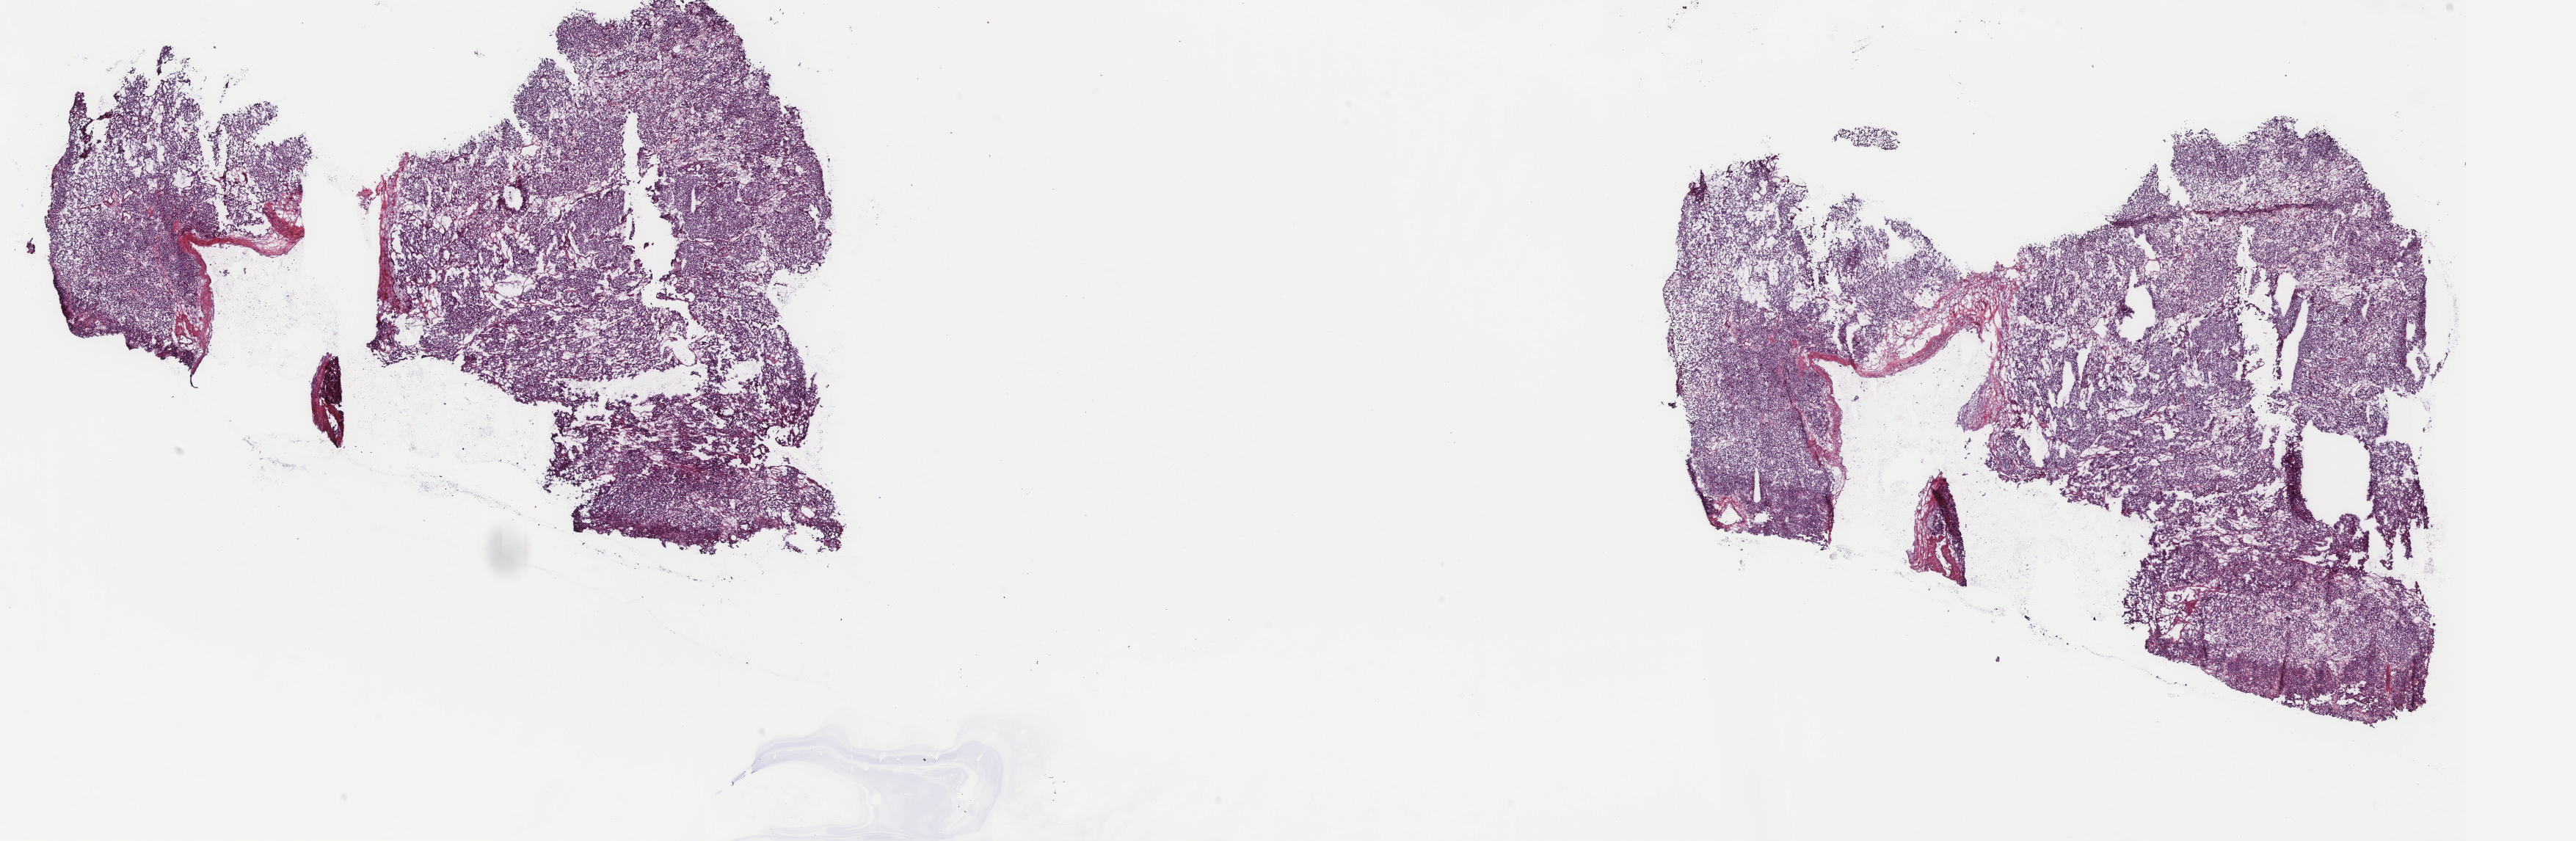
Hematoxylin and eosin (H&E) stained whole-slide image, low-resolution overview of the scanned area, about 27.9 x 9.1 mm; frozen section from the top of the tissue portion; sample: primary tumour, adrenal gland. Patient: male, age at initial diagnosis 48 years. Composition of this section per pathologist review: tumour cells 100%, tumour nuclei 80%, normal cells 0%, stromal cells 0%, necrosis 0%. Inflammatory infiltration, as recorded: lymphocyte infiltration 1%, monocyte infiltration 0%, neutrophil infiltration 0%.
- laterality: left
- histologic diagnosis: Pheochromocytoma, NOS (medulla of adrenal gland)